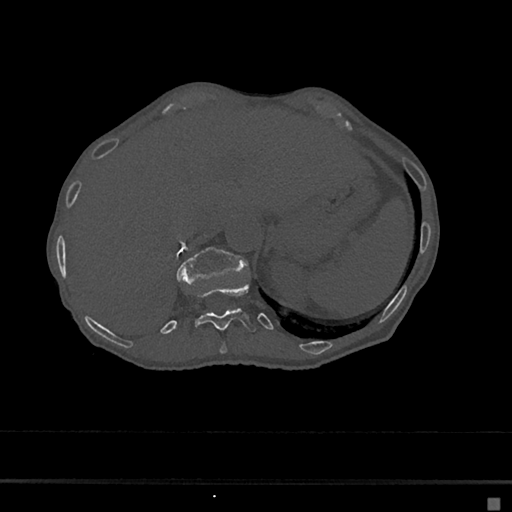
CT including the spine, one axial slice. Slice 166 of 797 in the series (ordered by position). Reconstruction kernel Br40s/3. Bone window (W 1800 / L 400 HU). 0.5 mm slice thickness. 512 × 512 image matrix, field of view 360 × 360 mm. Patient: female, 68 years. Case-level facts recorded for this patient, not image findings: primary cancer: renal.
Structures marked on this image (semi-automatically segmented with operator editing):
- T10 vertebra: bounding box (x1, y1, x2, y2) in pixels: (220, 342, 228, 354)
- T11 vertebra: (194, 283, 257, 332)
- T12 vertebra: (176, 247, 248, 284)